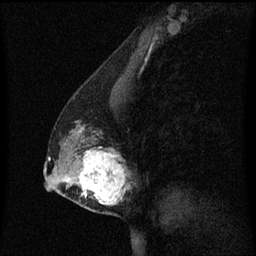
Breast MRI (dynamic contrast-enhanced), one sagittal slice. Position 28 of 60 along the scan axis. Dynamic contrast-enhanced series, image 2 of 3 at this slice position (ordered by acquisition). 1.5 T. TE 4.2 ms, TR 8.4 ms. 2 mm slice thickness. 256 × 256 image matrix, field of view 200 × 200 mm. Female patient, age 40 years. From the clinical record (not read from this slice): setting: breast cancer imaged before/during neoadjuvant chemotherapy; receptor status: triple-negative.
Outlined on this slice (semi-automatically segmented with operator editing):
- analysis volume of interest (the breast-tissue region the enhancement analysis was run in; not a lesion): box from (x=60, y=104) to (x=133, y=215) px
- tumour enhancement mask (voxels above the 70 % enhancement threshold inside the analysis volume of interest): (x=64, y=128)–(x=129, y=205)